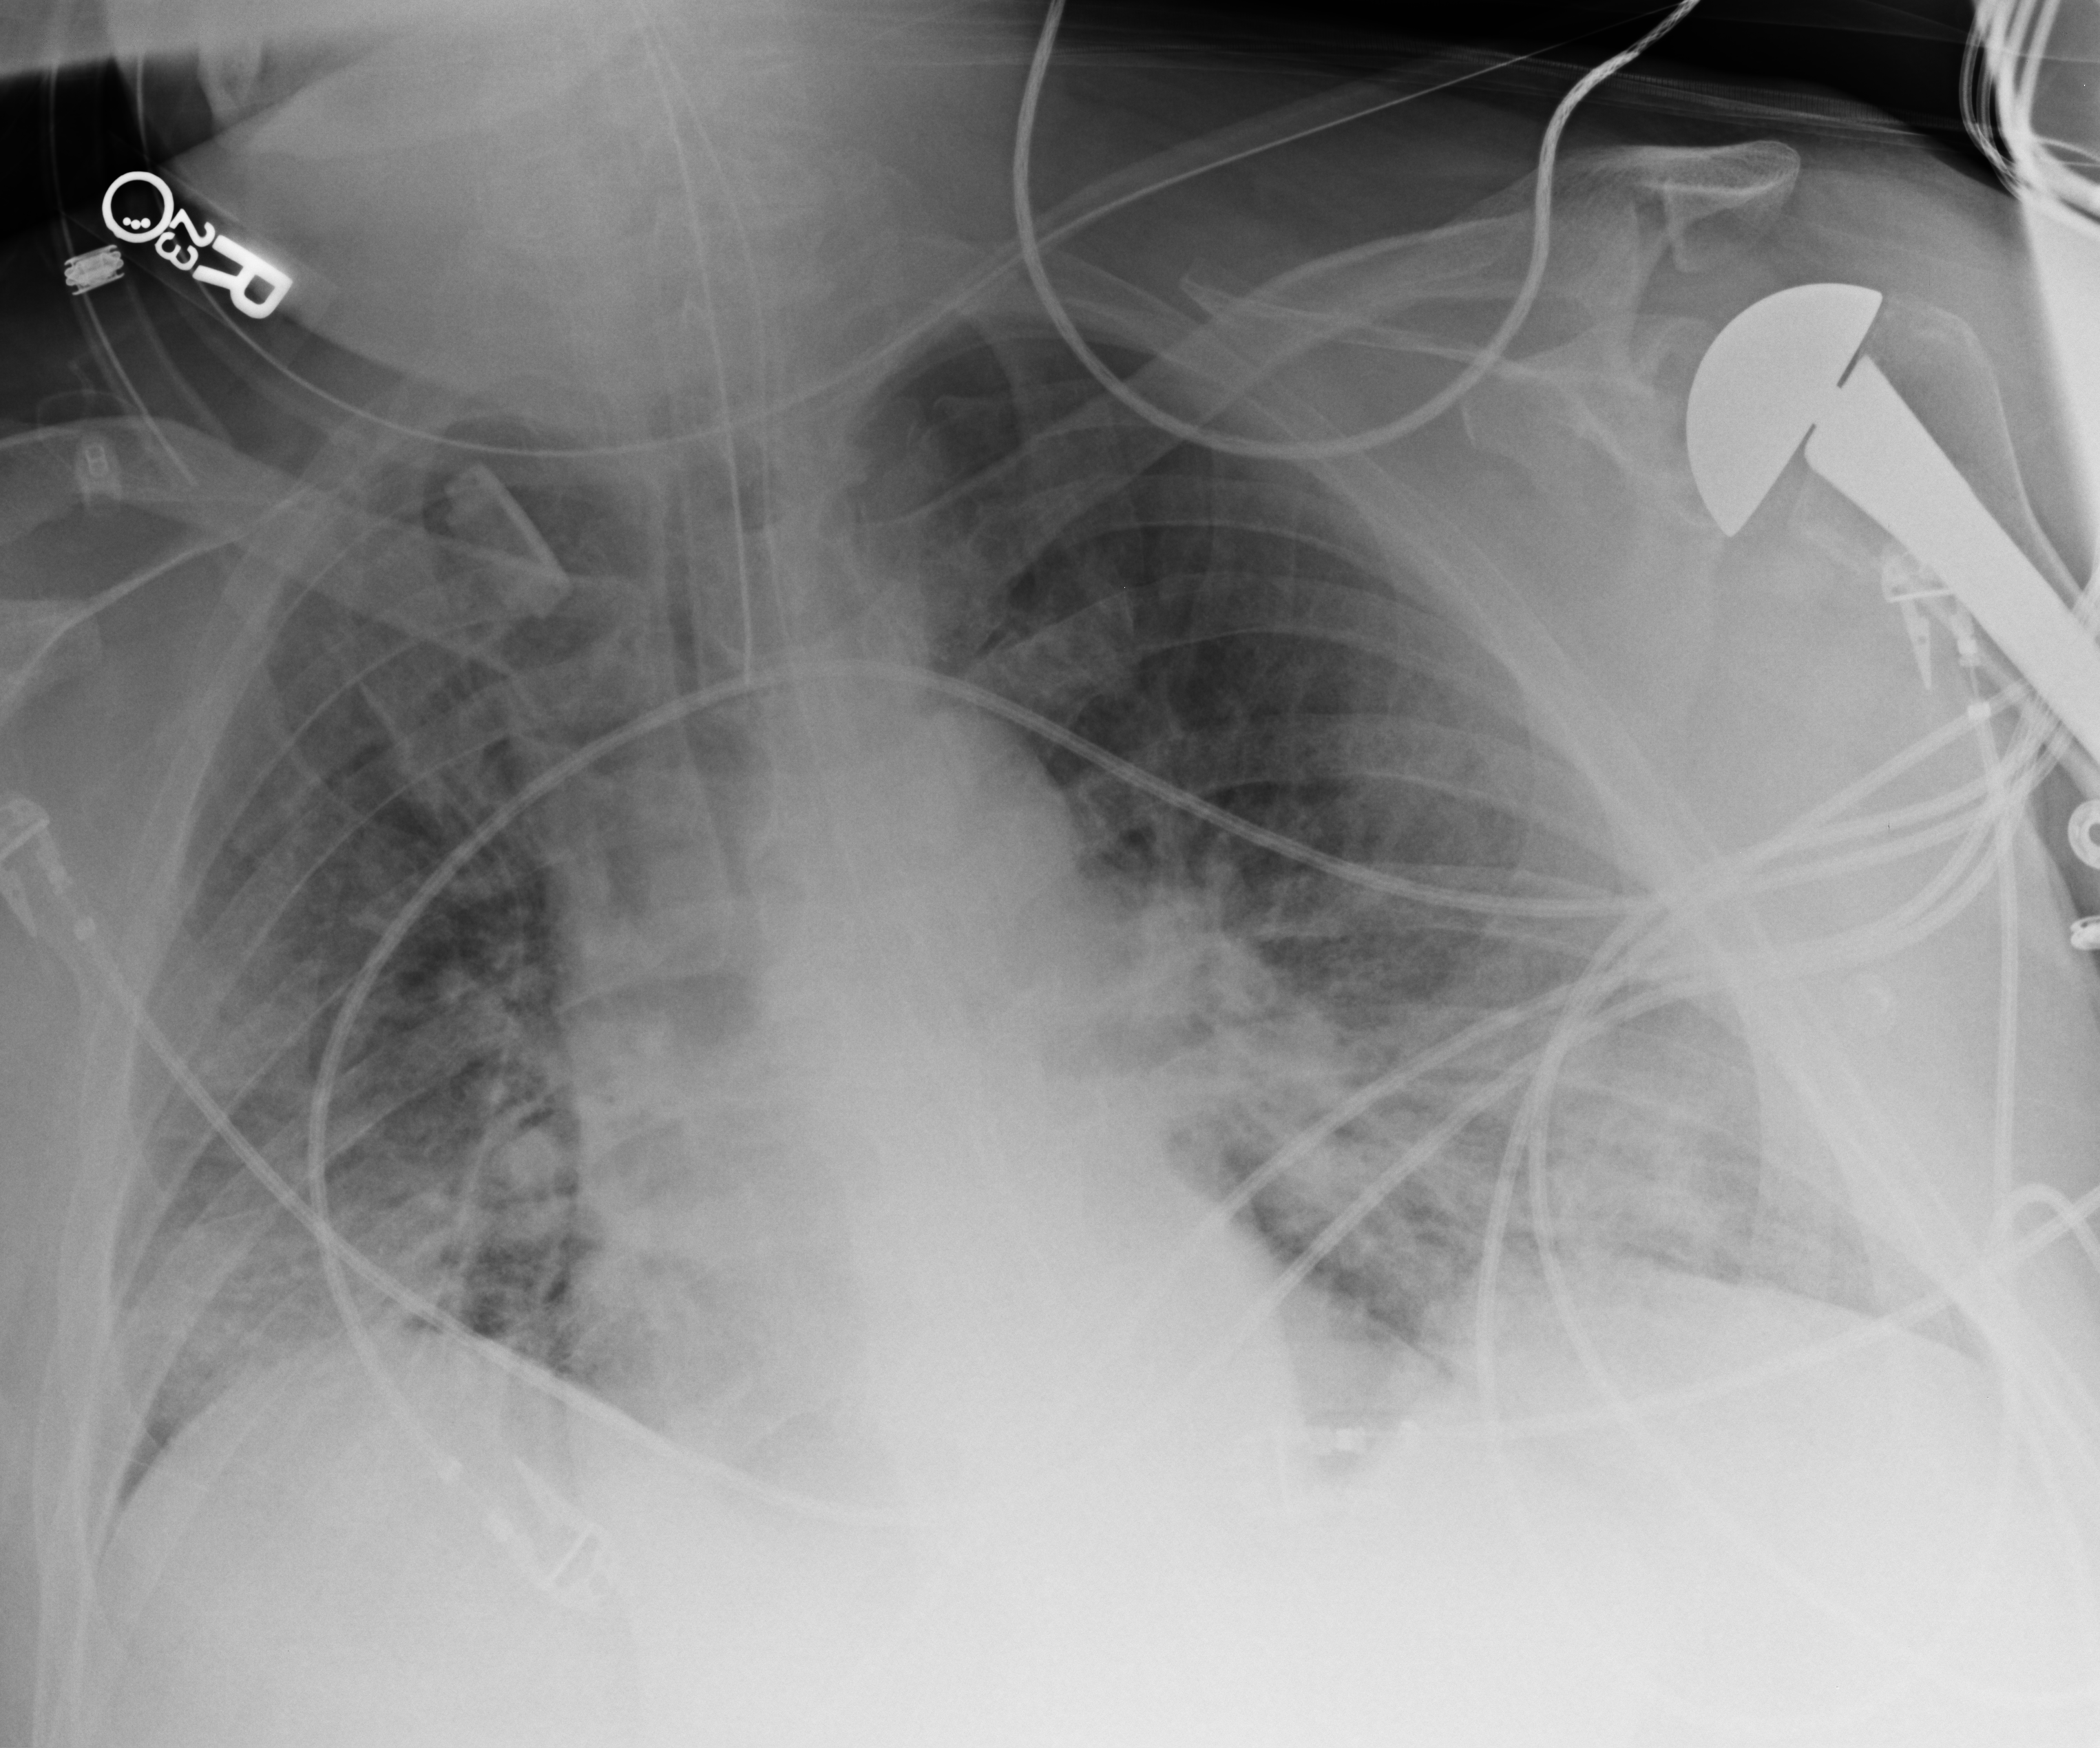
Portable chest radiograph. Patient hospitalised with COVID-19; male, aged 60–74 years.
Hospital-stay facts (about this admission, not read from this image; timing relative to this image not recorded): mechanically ventilated during this hospital stay: yes.